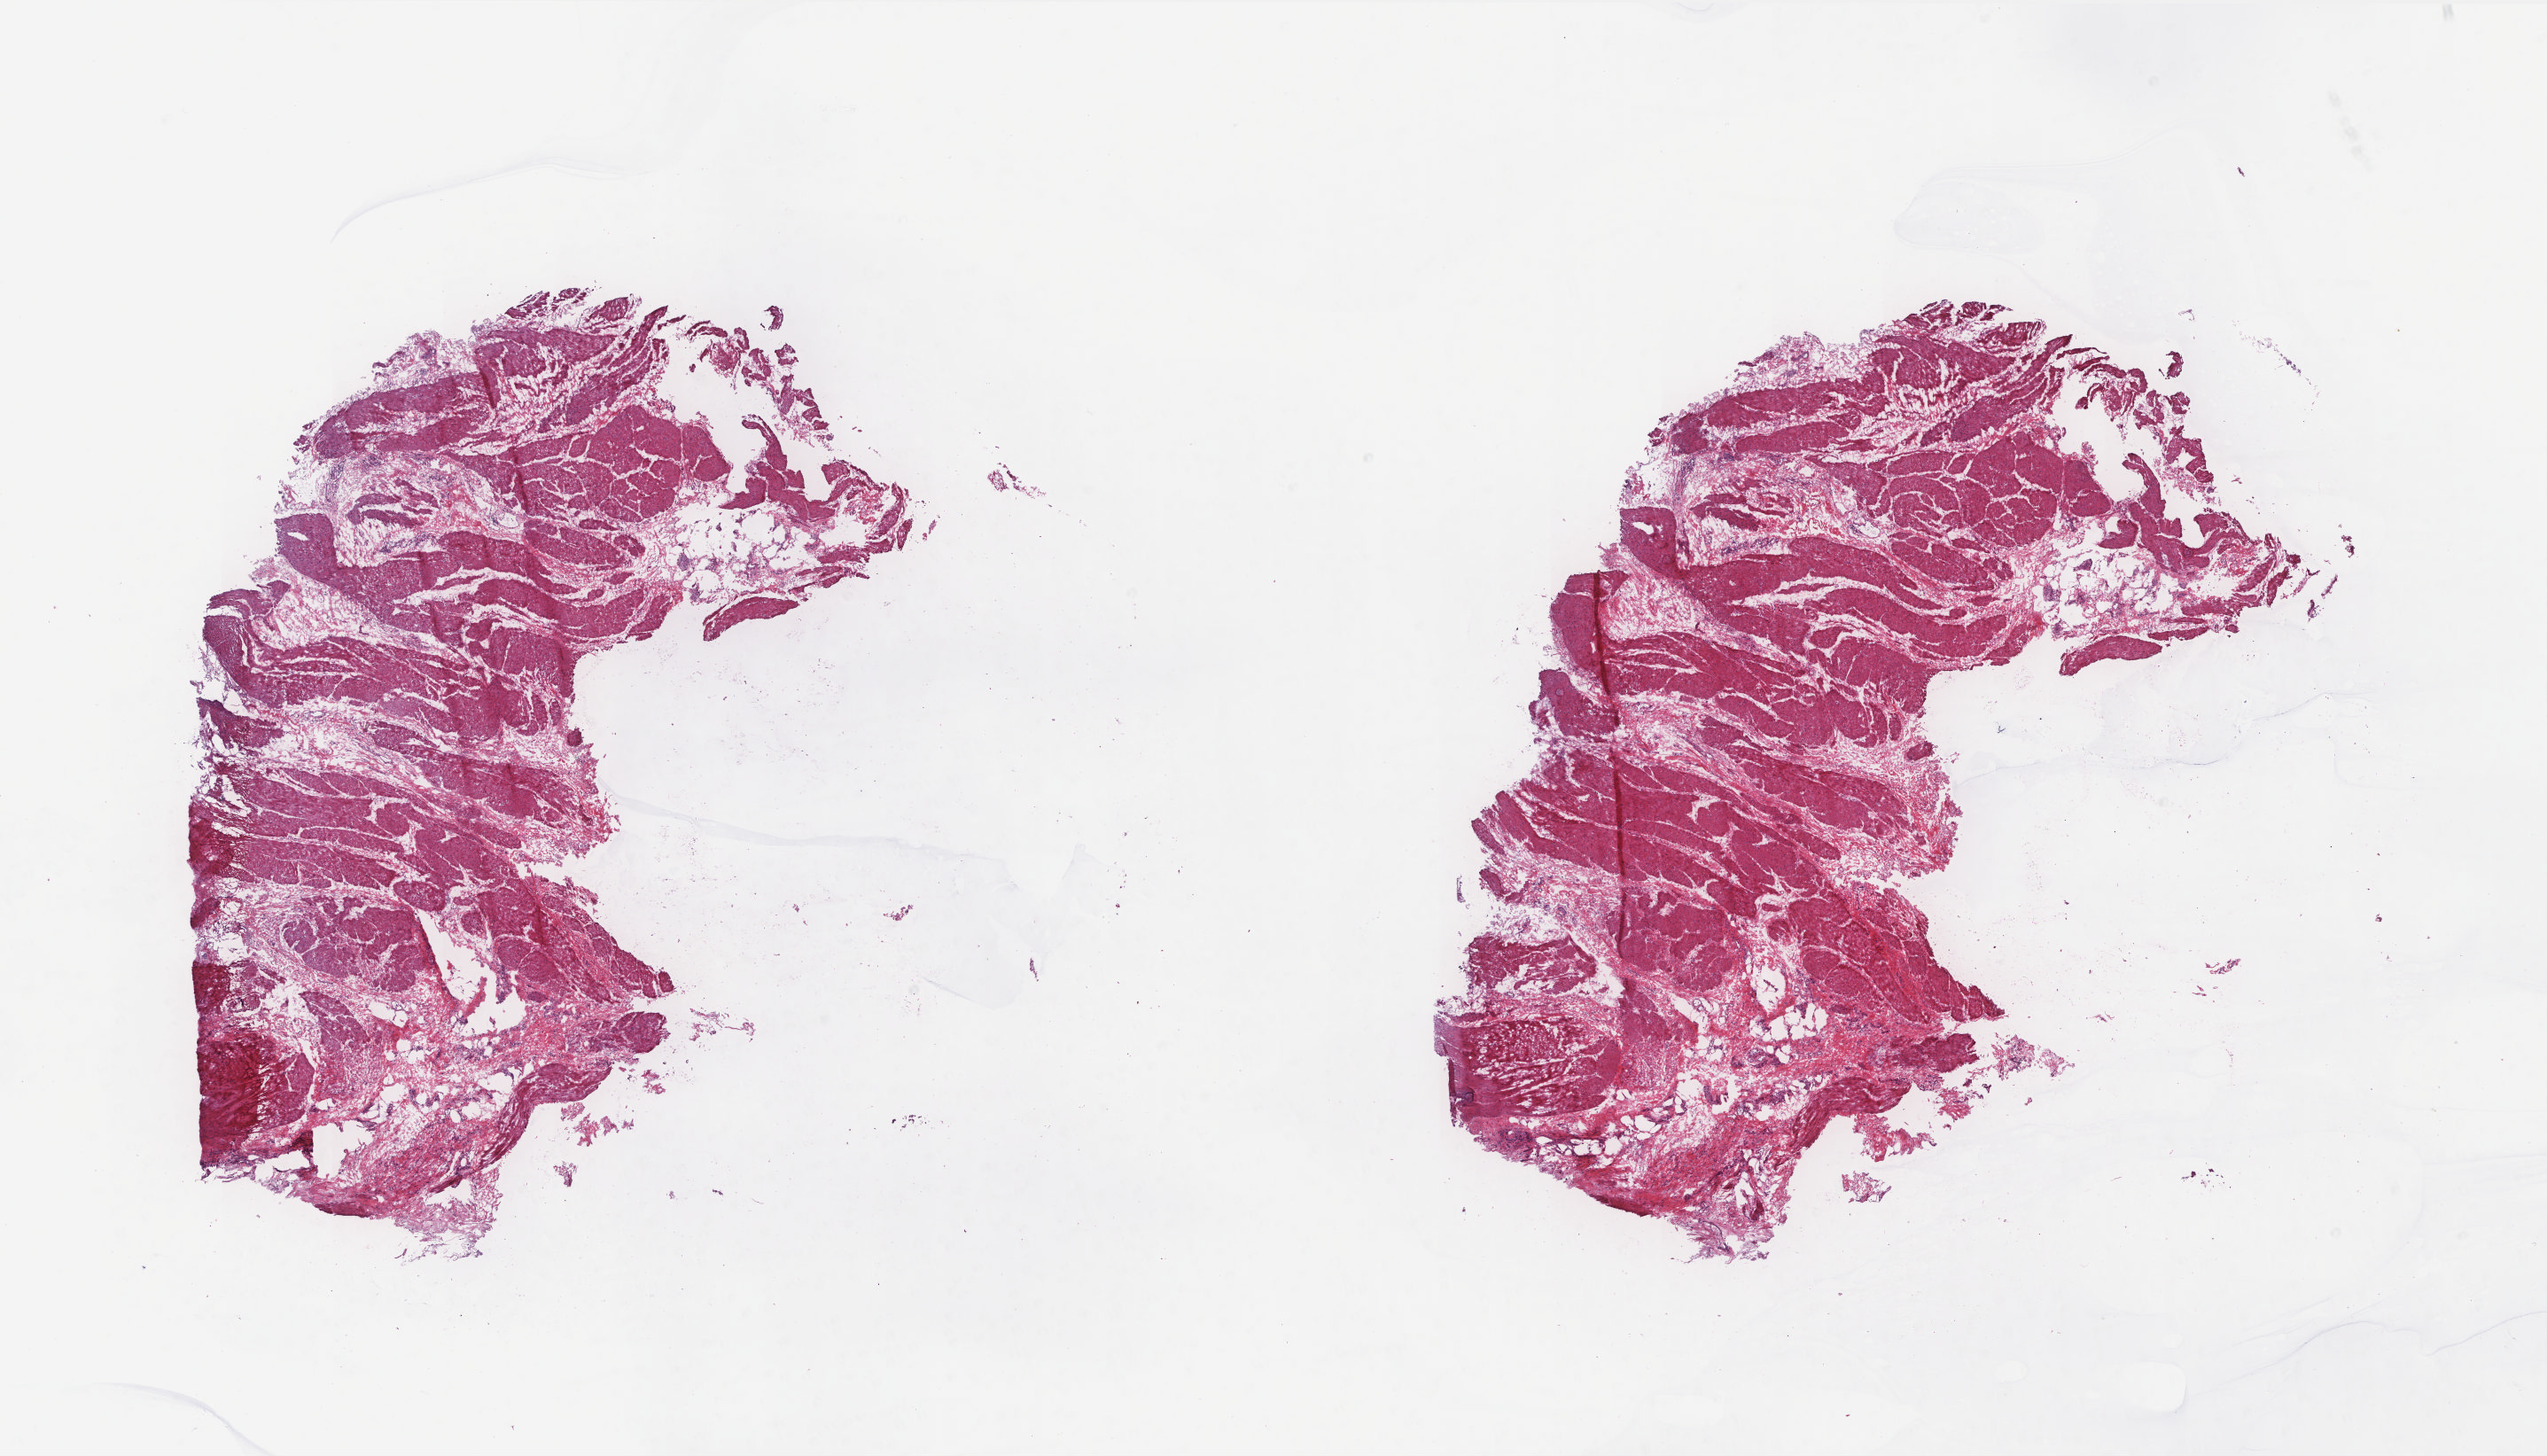
Whole-slide histology image, H&E-stained, low-resolution overview of the scanned area, about 23.0 x 13.1 mm (slide scanned at 20x), frozen section from the top of the tissue portion, sample: solid tissue normal (non-tumour tissue), bladder. Male, age 65 years at initial diagnosis. Pathologist review of this section (percent, as recorded): tumour cells 0%, tumour nuclei 0%, normal cells 70%, stromal cells 30%, necrosis 0%. Infiltration values recorded for this section: lymphocyte infiltration 1%, monocyte infiltration 0%, neutrophil infiltration 0%.
- this section: solid tissue normal (non-tumour) sample from the same patient
- patient diagnosis: Transitional cell carcinoma (posterior wall of bladder)